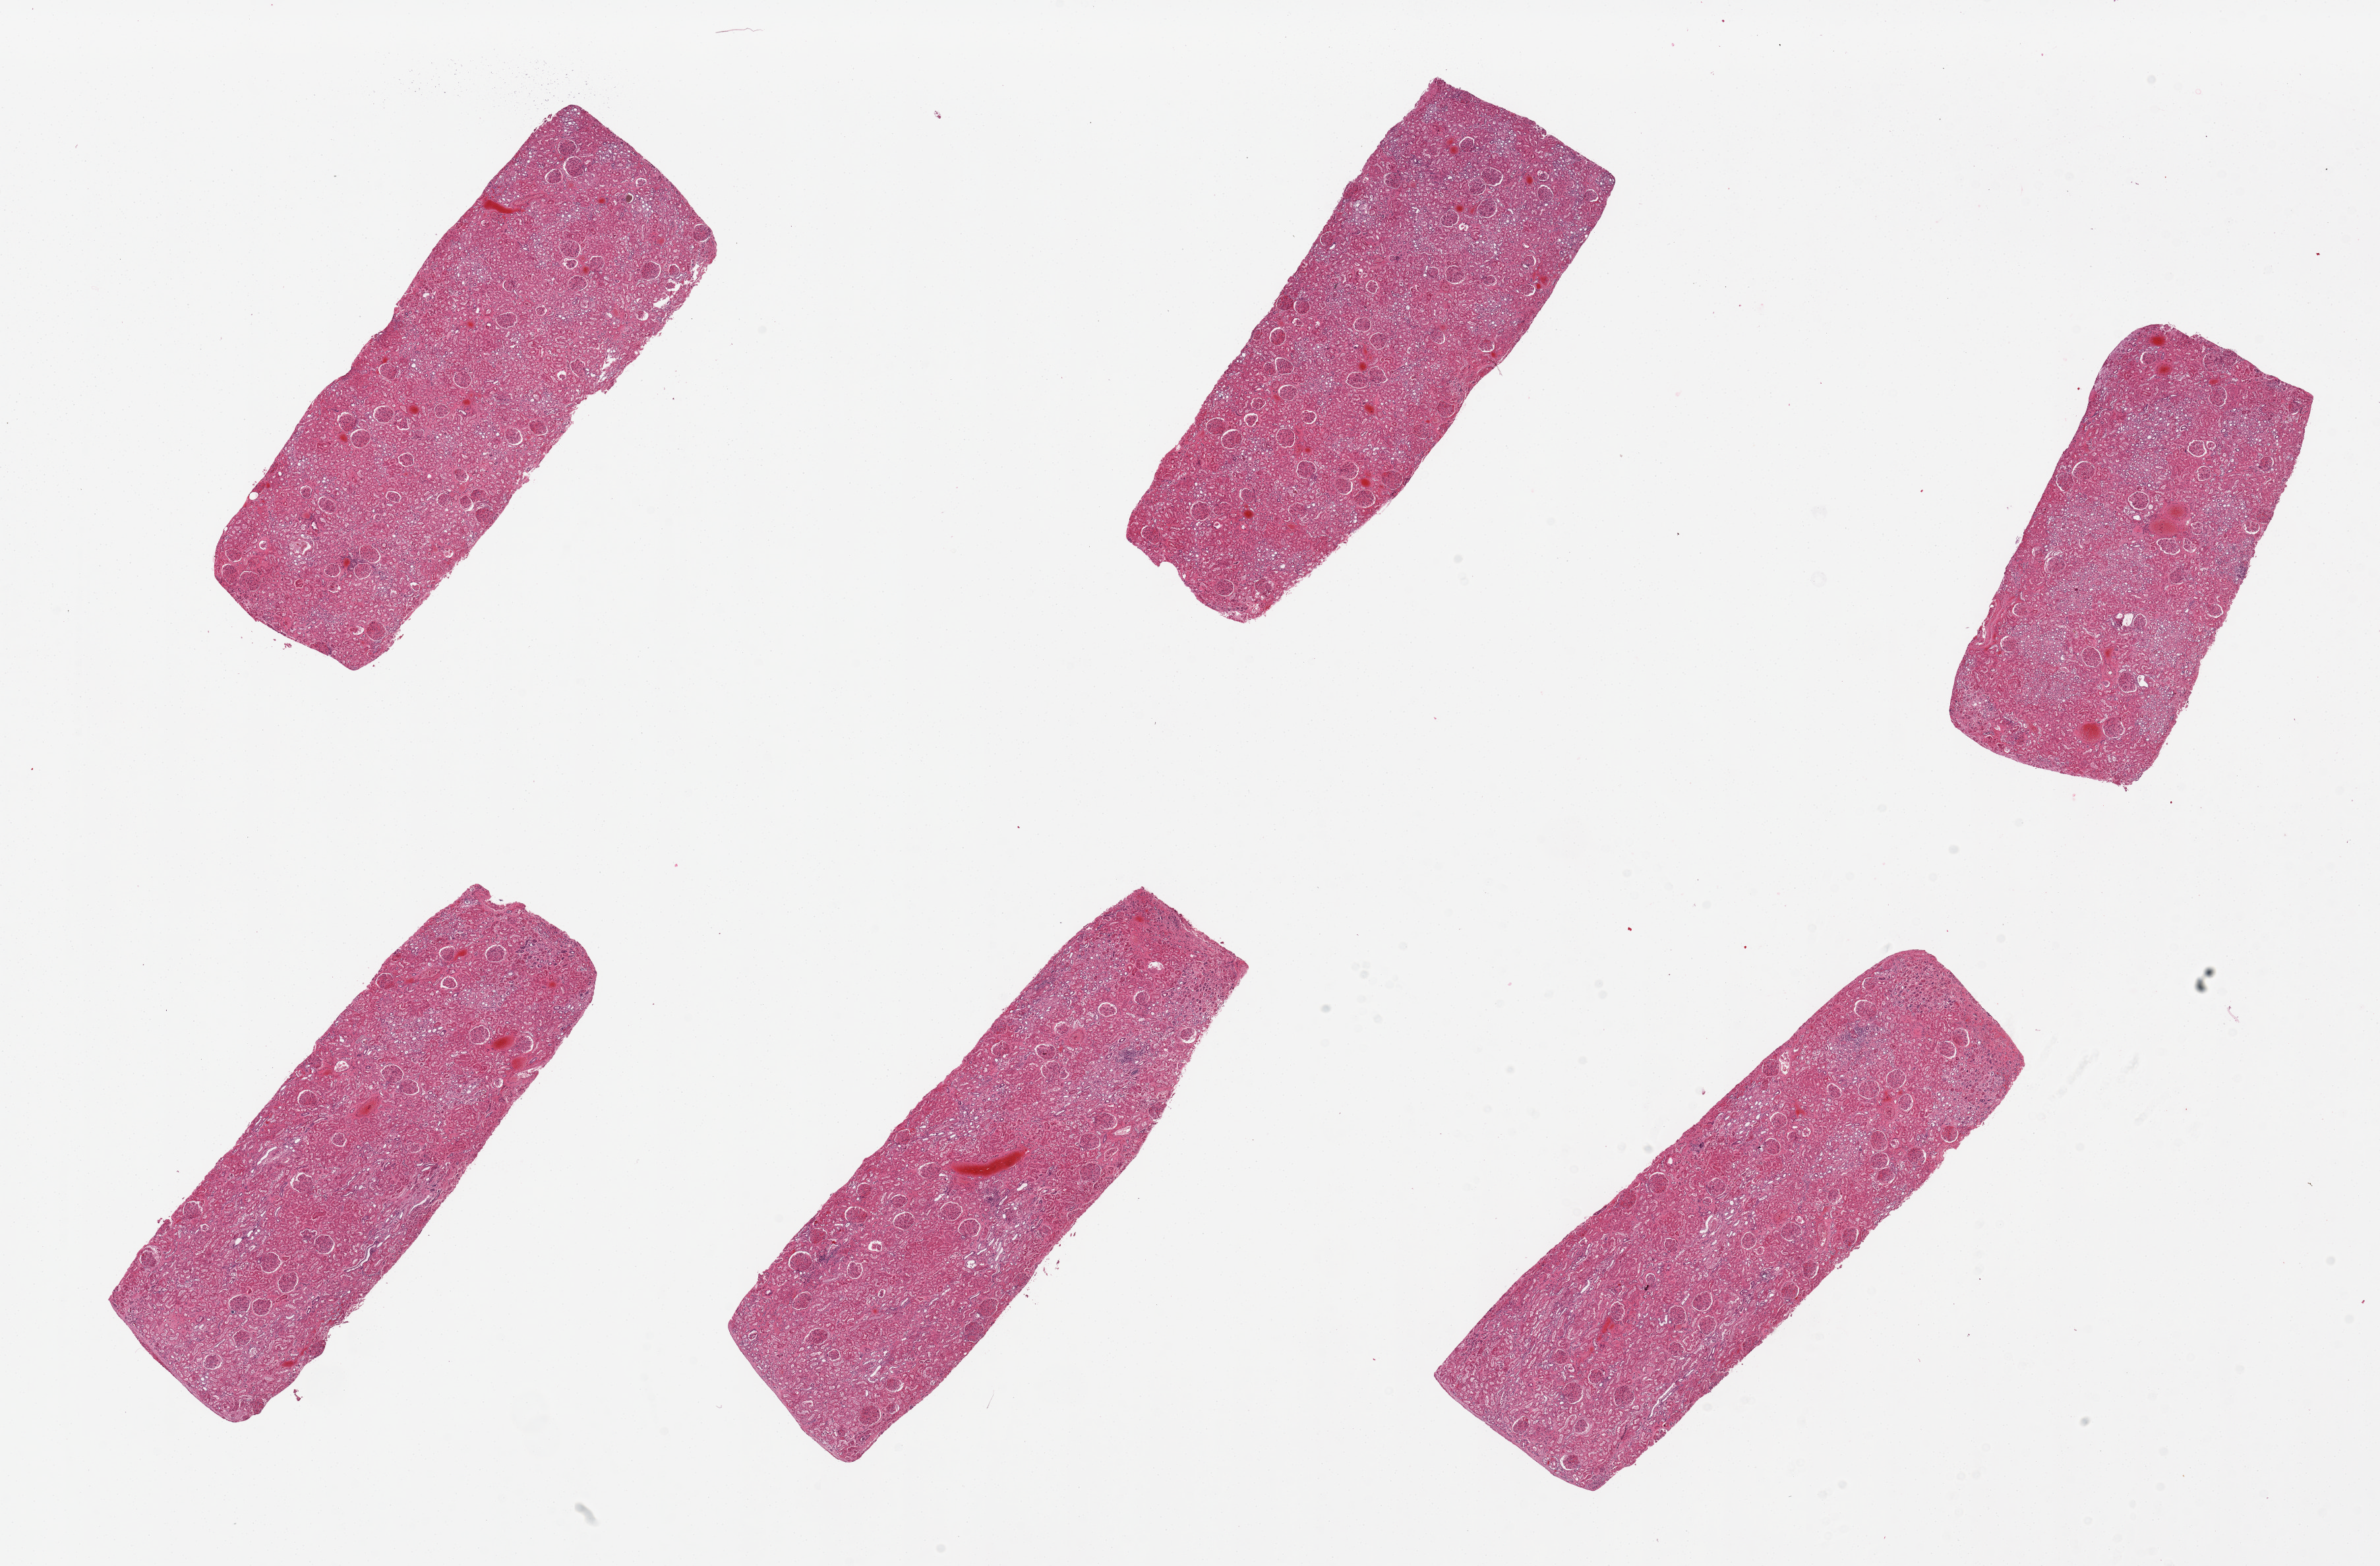
Haematoxylin and eosin whole-slide image, brightfield, a low-resolution overview of the entire scanned area, about 28.5 x 18.8 mm (slide scanned at 20x). PAXgene-fixed paraffin-embedded (PFPE) section. Sampled site (target tissue): renal cortex. Donor tissue sample. Donor: male.
Reviewer comment on this tissue sample: 6 pieces. Well sampled cortex without lesions.